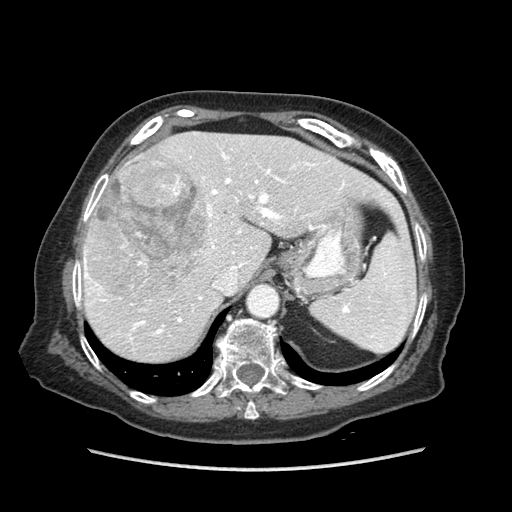
Contrast-enhanced abdominal CT (liver protocol), one axial slice. Position 59 of 89 along the scan axis. Soft-tissue window (W 400 / L 40 HU). 2.5 mm slice thickness. 512 × 512 image matrix, field of view 360 × 360 mm. From the clinical record (not read from this slice): diagnosis: hepatocellular carcinoma (patient treated with transarterial chemoembolisation; whether this scan precedes or follows treatment is not stated here); TNM stage (as recorded): Stage-IIIA; Child-Pugh class: A.
Annotated regions visible in this slice (semi-automatic segmentation, software-assisted and operator-edited):
- liver parenchyma outside the tumour (the mass and vessels are separate outlines, so this box may not span the whole liver): box from (x=78, y=132) to (x=396, y=362) px
- mass: (x=85, y=160)–(x=206, y=304)
- liver vessels: (x=84, y=149)–(x=383, y=340)